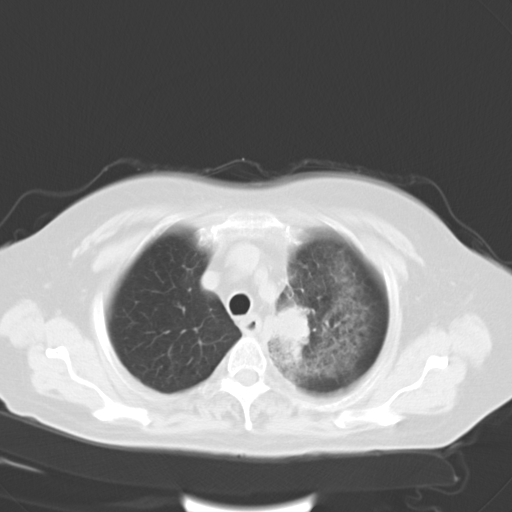
Chest CT, one axial slice. Reconstruction kernel B40f. Lung window (W 1500 / L -600 HU). 10 mm slice thickness. 512 × 512 image matrix, field of view 353 × 353 mm. Patient: female, 65 years. Case-level facts recorded for this patient, not image findings: clinical TNM (as recorded): T2b N1 M0.
Annotated regions visible in this slice (bounding box drawn by a radiologist):
- lung tumour (recorded histology: adenocarcinoma): bounding box (x1, y1, x2, y2) in pixels: (269, 304, 319, 366)